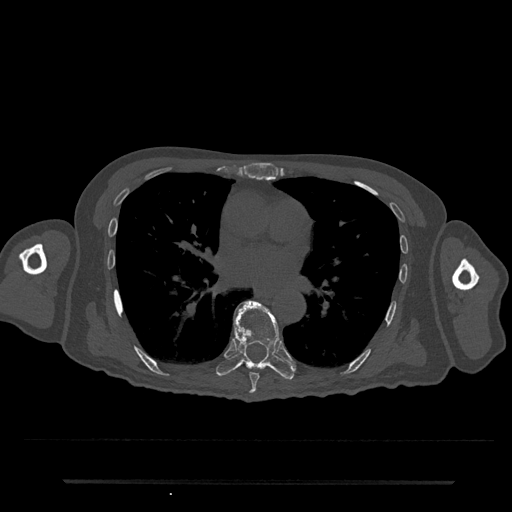
CT including the spine, one axial slice. Position 443 of 797 along the scan axis. Reconstruction kernel Br40s/3. Bone window (W 1800 / L 400 HU). 0.5 mm slice thickness. 512 × 512 image matrix, field of view 427 × 427 mm. Male patient, age 74 years. From the clinical record (not read from this slice): primary cancer: prostate.
Annotated regions visible in this slice (semi-automatic segmentation, software-assisted and operator-edited):
- T7 vertebra: bounding box <249,373,259,394> (left, top, right, bottom; pixels)
- T8 vertebra: <216,301,295,380>